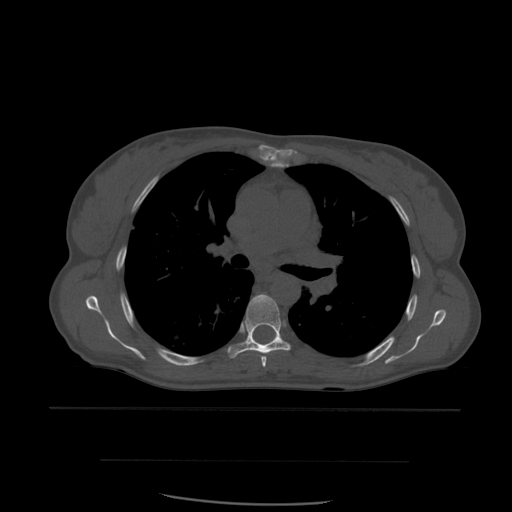
CT including the spine, one axial slice. Slice 396 of 574 in the series (ordered by position). Bone window (W 1800 / L 400 HU). 1.25 mm slice thickness. 512 × 512 image matrix. Patient age 48 years. Case-level facts recorded for this patient, not image findings: primary cancer: lung.
Outlined on this slice (semi-automatic segmentation, software-assisted and operator-edited):
- T5 vertebra: bounding box [x1, y1, x2, y2] px = [261, 356, 267, 368]
- T6 vertebra: [227, 294, 291, 359]